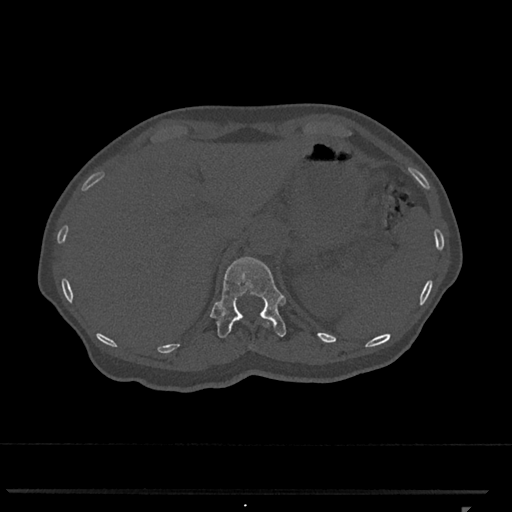
CT including the spine, one axial slice; position 475 of 793 along the scan axis; 120 kVp; bone window (W 1800 / L 400 HU); 0.5 mm slice thickness; 512 × 512 image matrix, field of view 380 × 380 mm. Female patient, age 62 years. Case-level facts recorded for this patient, not image findings: primary cancer: renal.
Outlined on this slice (semi-automatic segmentation, software-assisted and operator-edited):
- T11 vertebra: bounding box <266,324,269,326> (left, top, right, bottom; pixels)
- T12 vertebra: <216,257,286,338>